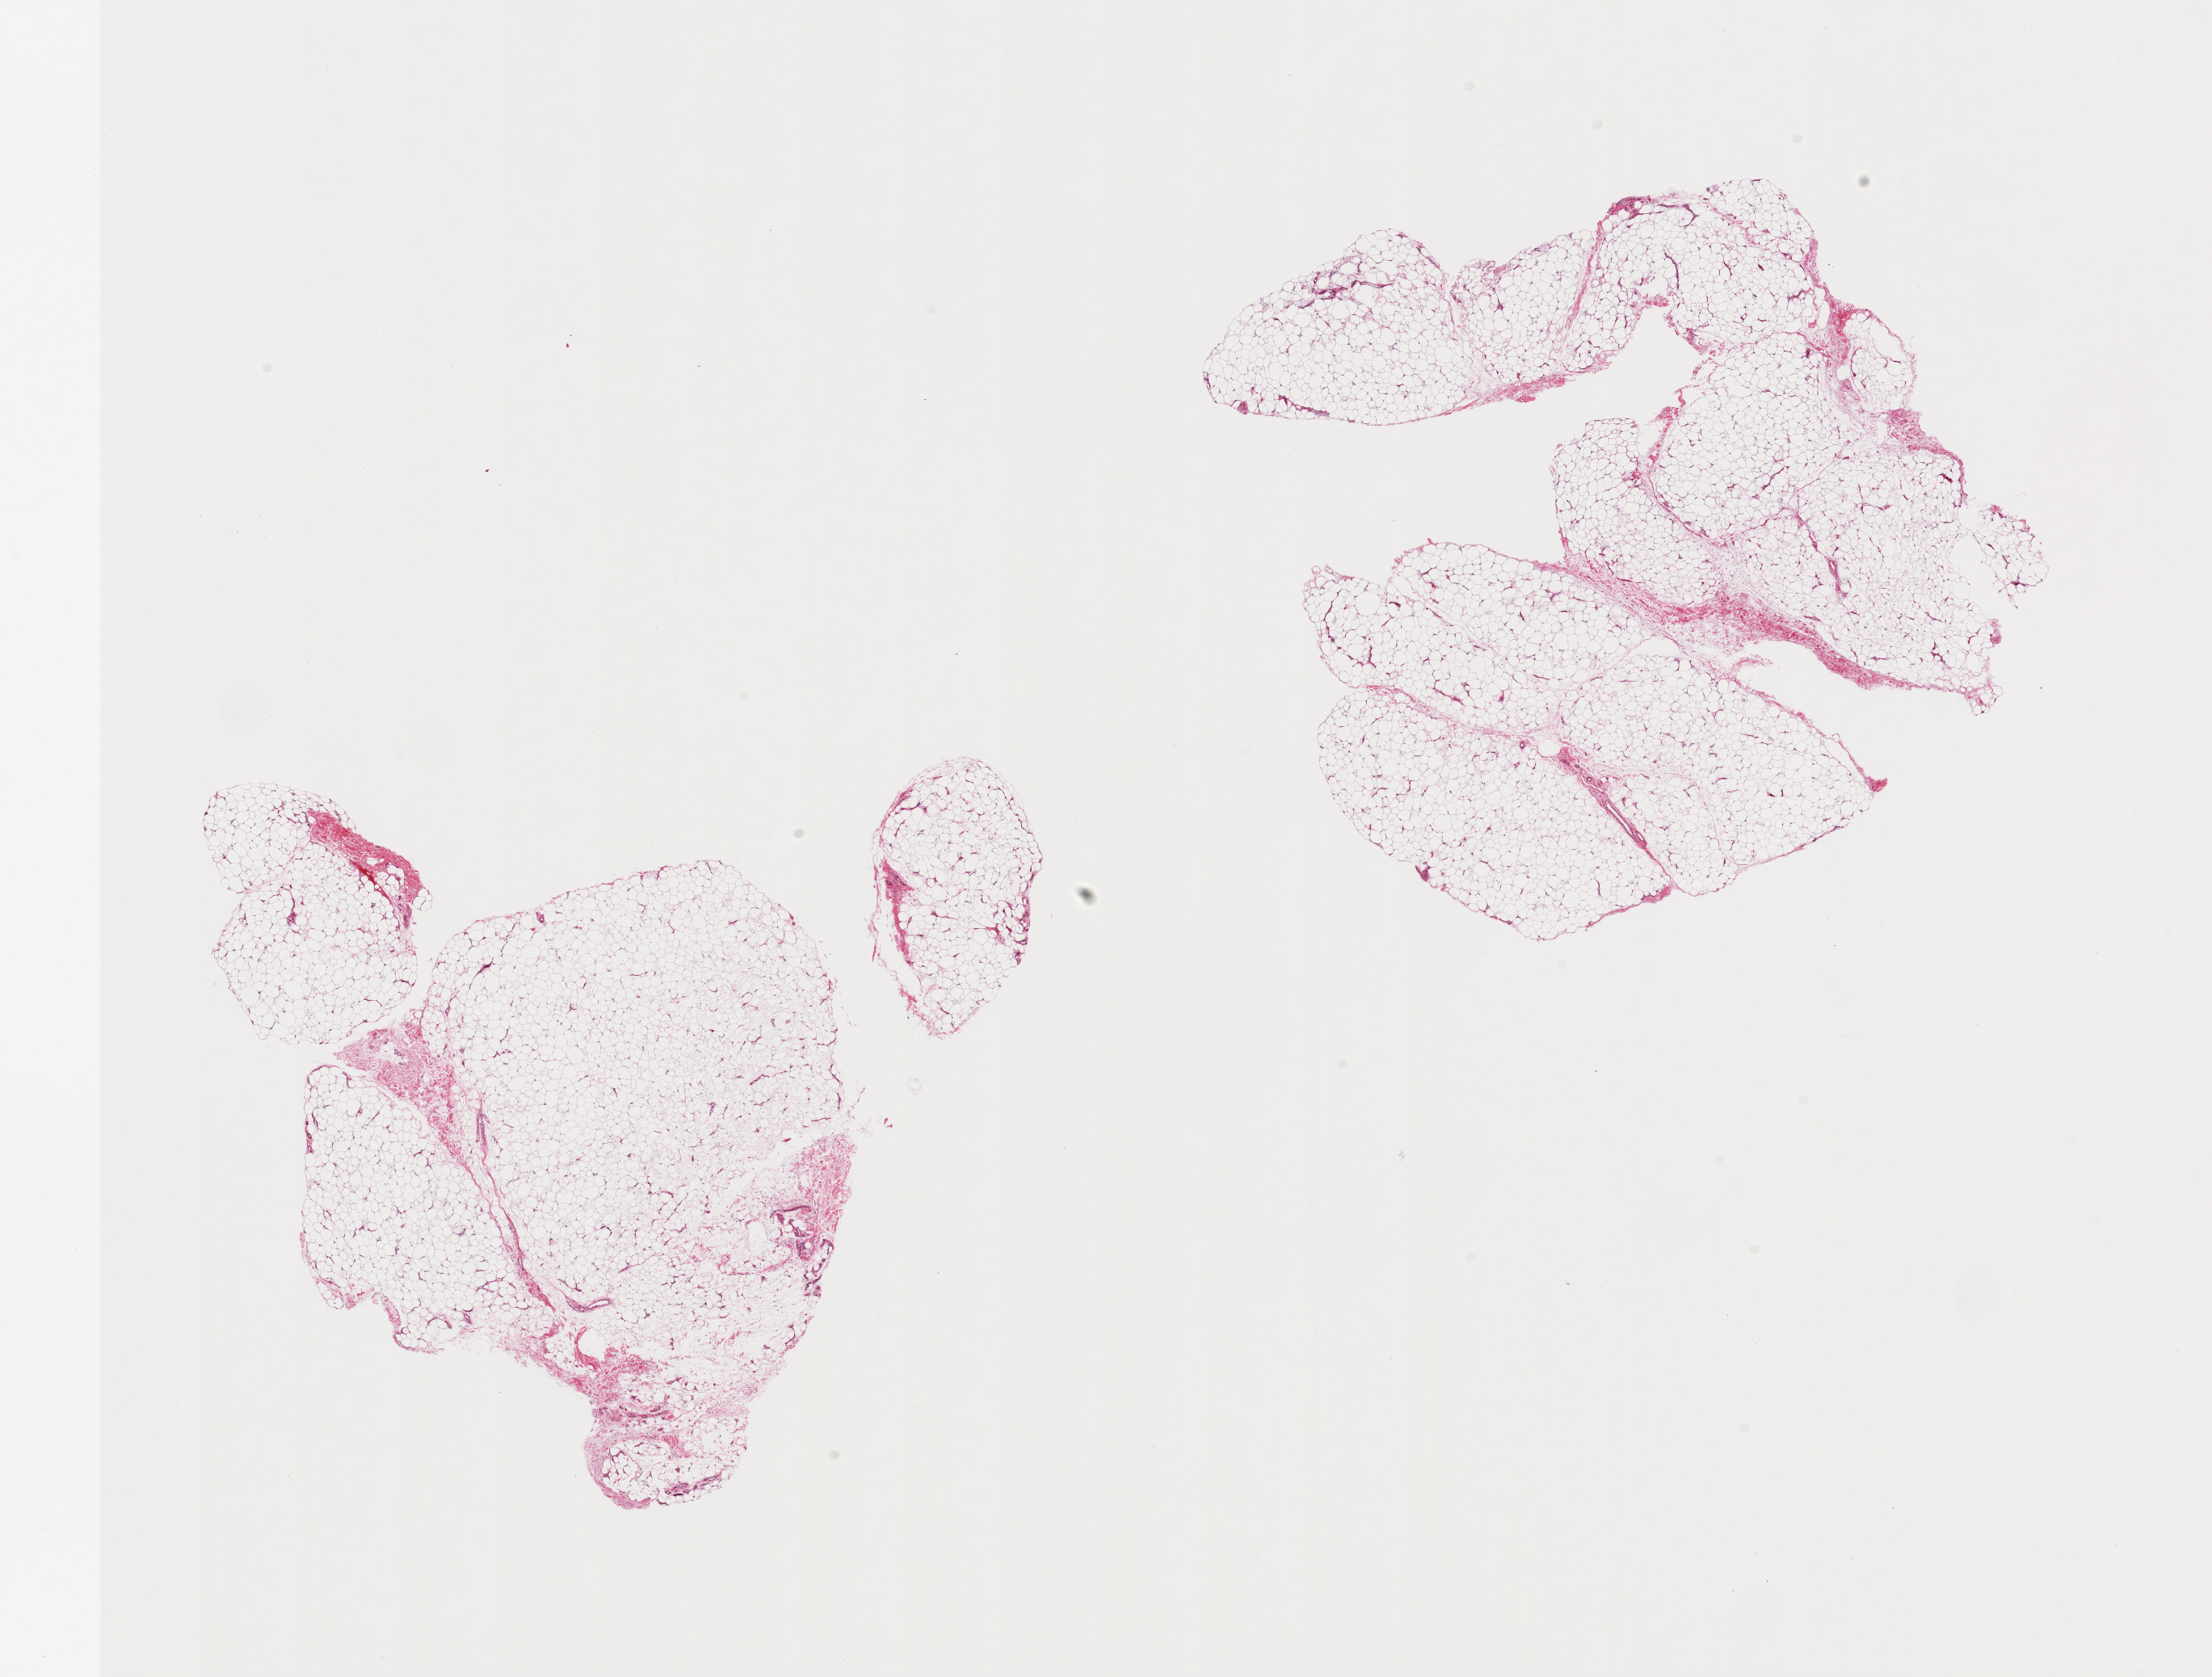
Digitized haematoxylin and eosin-stained section — shown as a low-resolution overview of the whole scanned area (about 21.7 x 16.4 mm, acquisition: 20x scan); PAXgene-fixed paraffin-embedded (PFPE) section; sampled site (target tissue): adipose tissue; tissue donor sample. Male donor.
Pathologist's review note for this sample: 2 pieces, ~5-10% fascia/vascular elements.